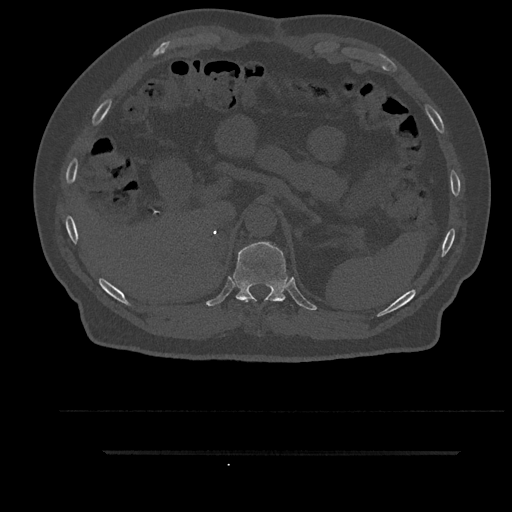
CT including the spine, one axial slice; slice 324 of 797 in the series (ordered by position); bone window (W 1800 / L 400 HU); 0.5 mm slice thickness; 512 × 512 image matrix, field of view 432 × 432 mm. Male patient, age 63 years. Case-level facts recorded for this patient, not image findings: primary cancer: renal; vertebrae with lytic lesions (as recorded): T8.
Annotated regions visible in this slice (semi-automatically segmented with operator editing):
- T11 vertebra: box from (x=233, y=242) to (x=288, y=302) px